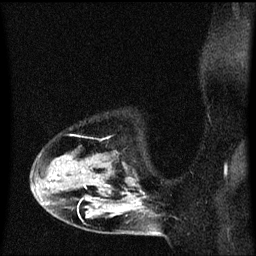
Breast MRI (dynamic contrast-enhanced), one sagittal slice. Slice 44 of 60 in the series (ordered by position). Dynamic contrast-enhanced series, image 2 of 3 at this slice position (ordered by acquisition). 1.5 T. TE 4.2 ms, TR 8.4 ms. 2 mm slice thickness. 256 × 256 image matrix. Female patient, age 49 years. From the clinical record (not read from this slice): setting: breast cancer imaged before/during neoadjuvant chemotherapy; receptor status: HR-positive, HER2-negative.
Annotated regions visible in this slice (semi-automatically segmented with operator editing):
- analysis volume of interest (the breast-tissue region the enhancement analysis was run in; not a lesion): box from (x=32, y=138) to (x=160, y=221) px
- tumour enhancement mask (voxels above the 70 % enhancement threshold inside the analysis volume of interest): (x=50, y=170)–(x=139, y=205)